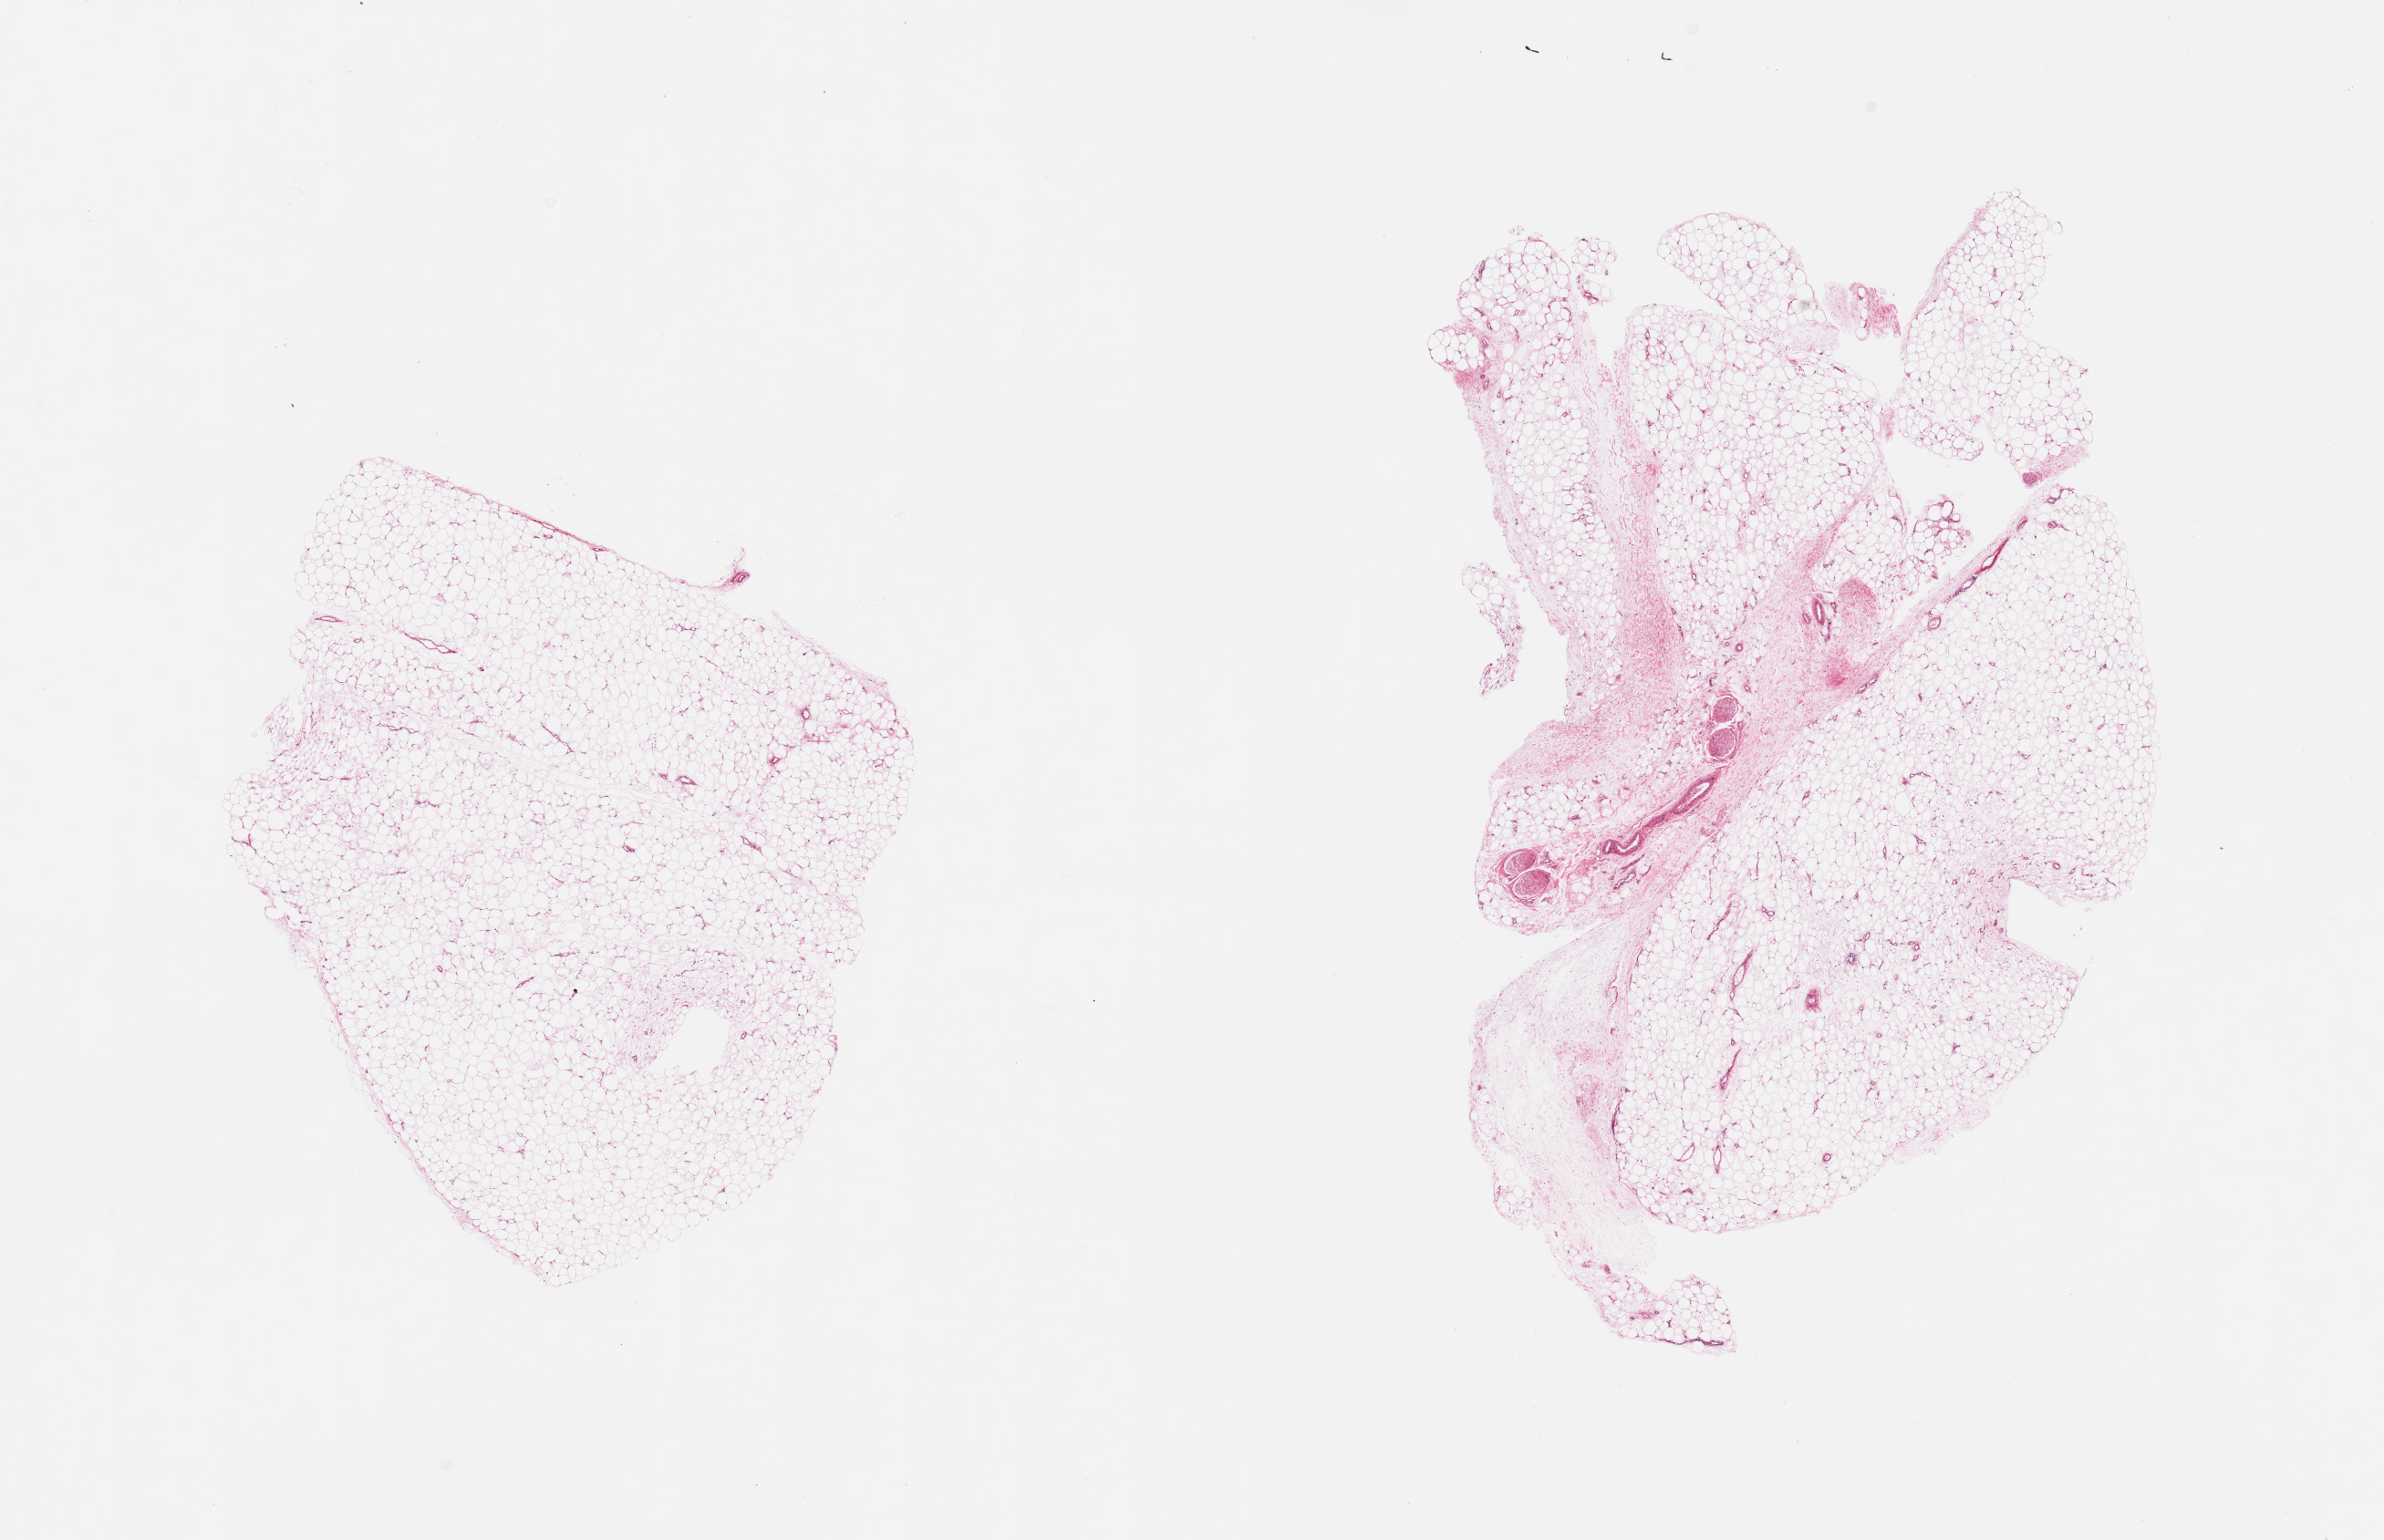
Whole-slide image, haematoxylin and eosin stain — shown as a low-resolution overview of the whole scanned area (about 20.7 x 13.4 mm, acquisition: 20x scan), PAXgene-fixed paraffin-embedded (PFPE) section, section of adipose tissue (target tissue), donor tissue sample. Donor: female.
Pathologist's review note for this sample: 2 pieces, ~5-10% non adipose elements, peripheral nerve, vascular elements.